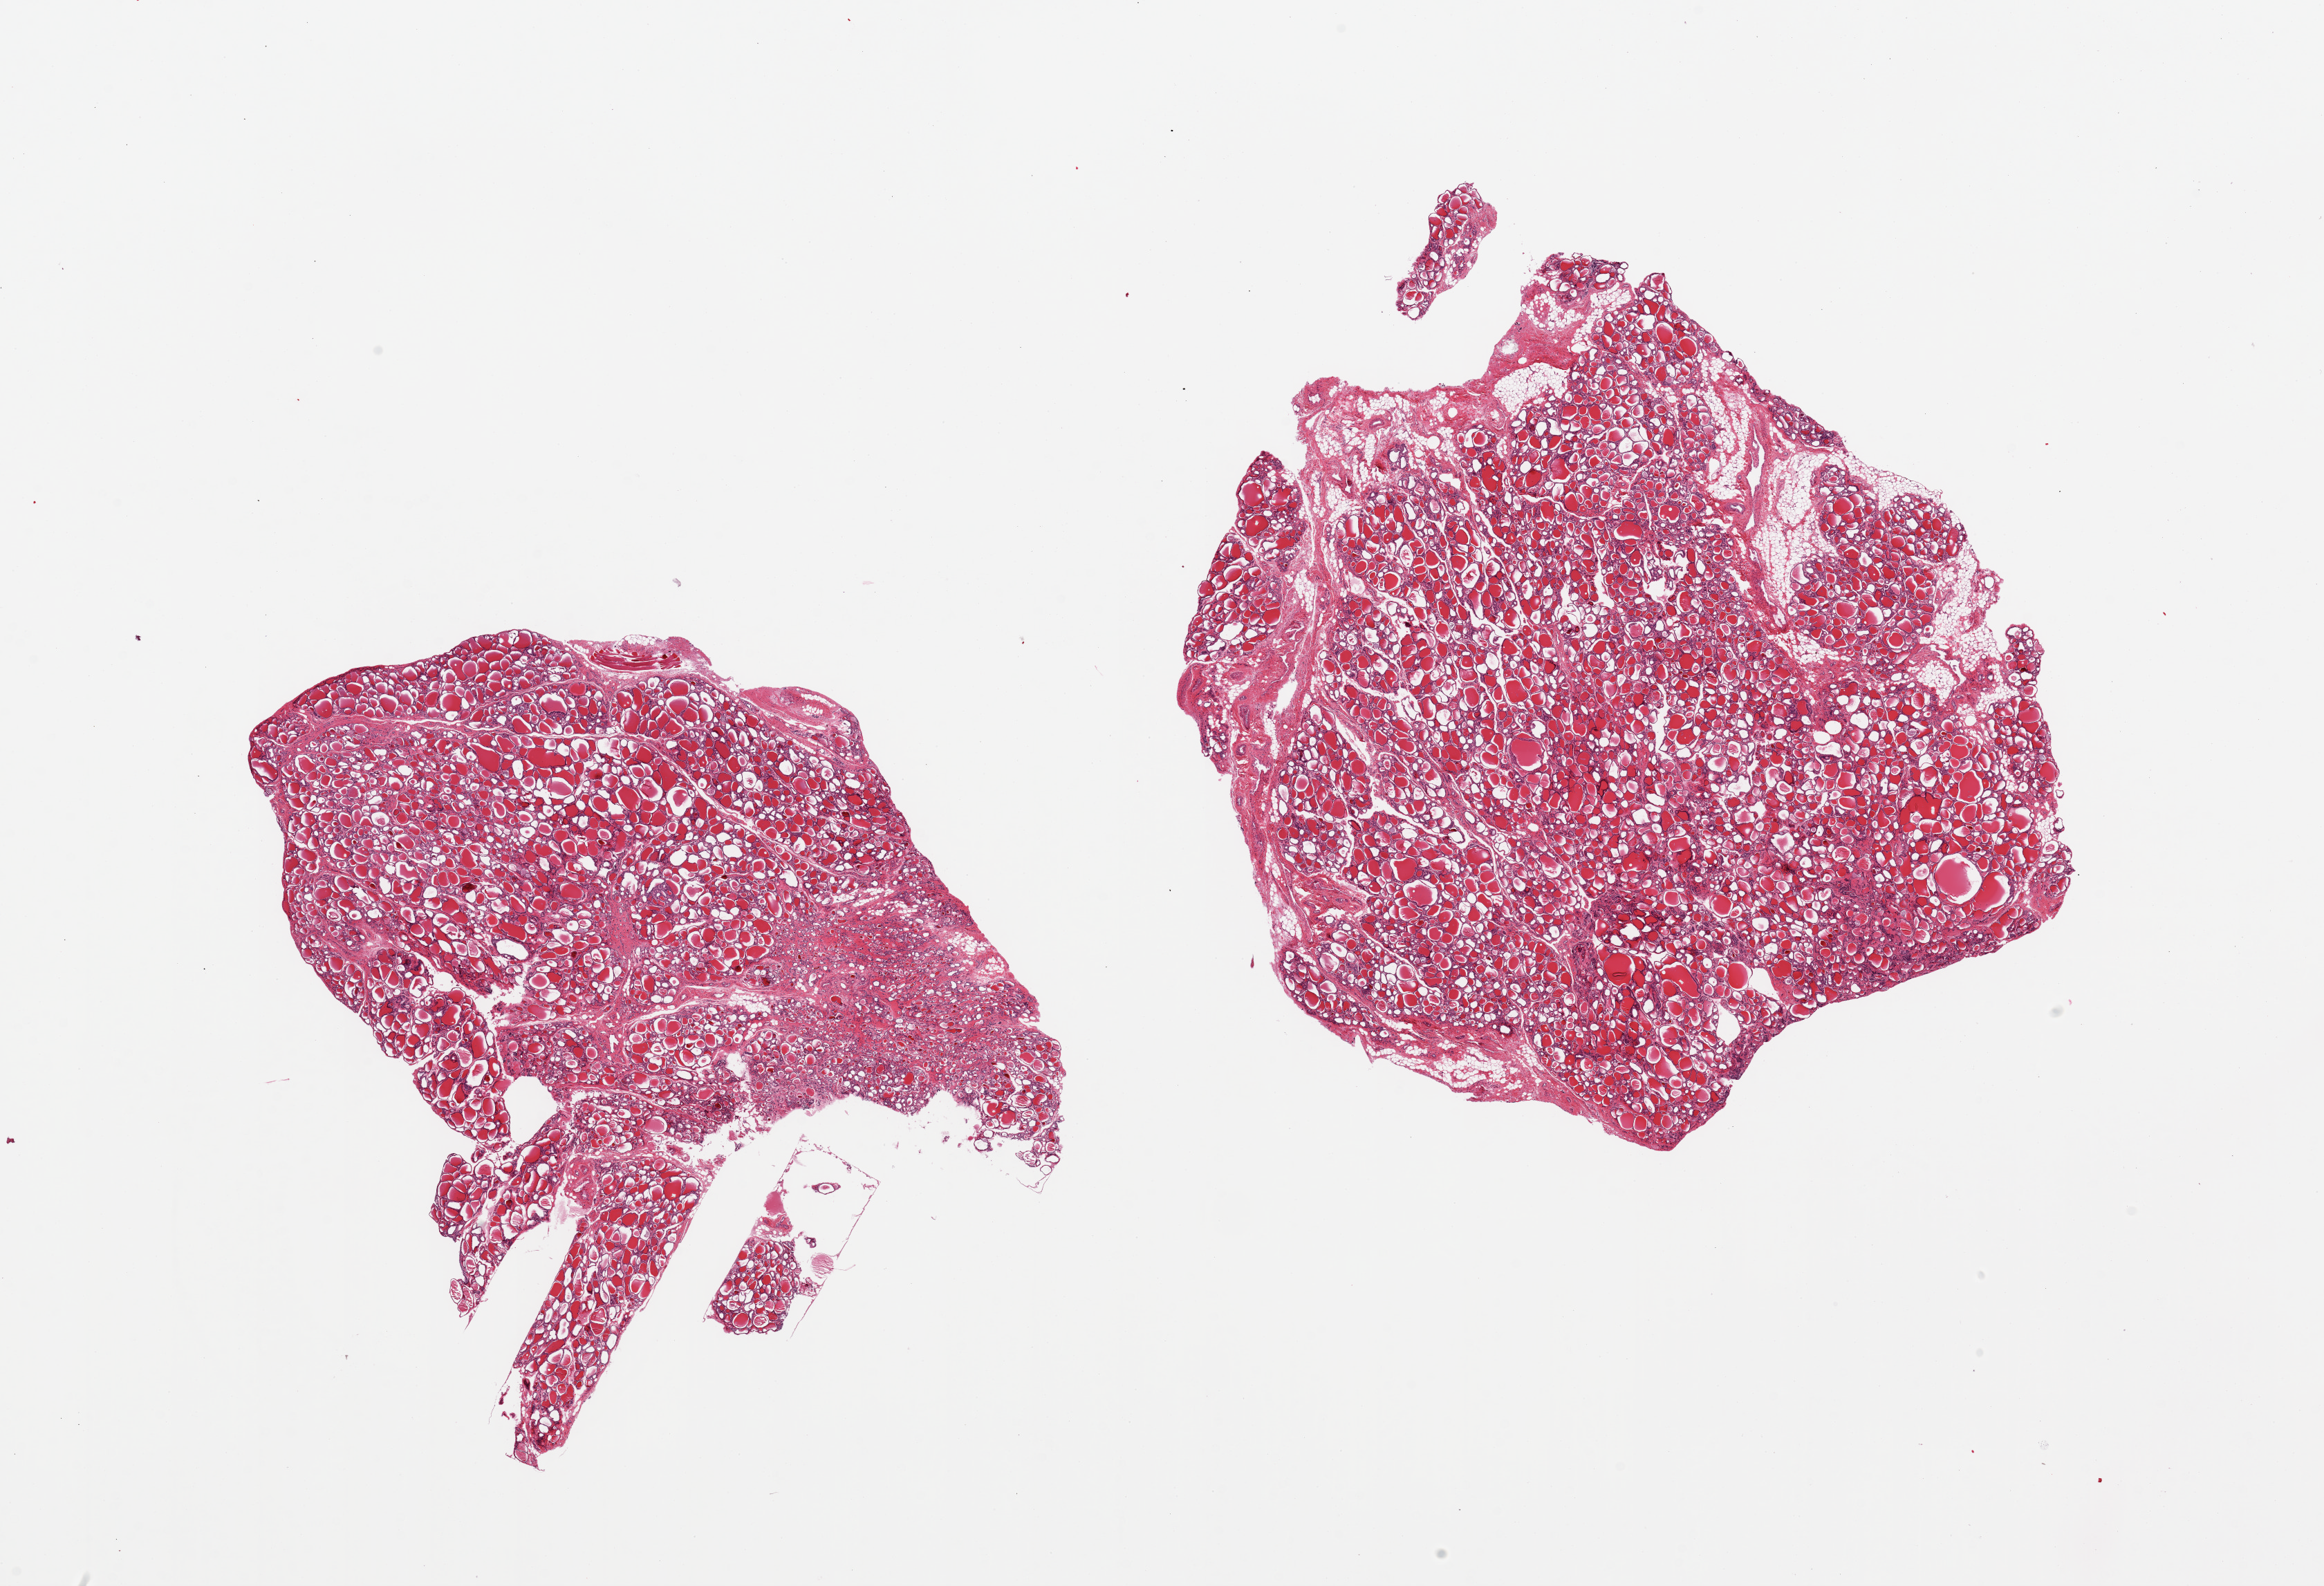
Whole-slide image, haematoxylin and eosin stain, low-resolution overview of the scanned area, about 26.6 x 18.1 mm (from a 20x scan), PAXgene-fixed, paraffin-embedded tissue, section of thyroid (target tissue), donor tissue sample. Donor: female.
Review note (as recorded): 2 pieces, small attachment of skeletal muscle, larger piece is ~15% fat and fibrovascular tissue.